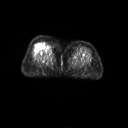
FDG PET of an extremity soft-tissue mass (from a PET/CT study), one axial slice; slice 23 of 267 in the series (ordered by position); 3.27 mm slice thickness; 128 × 128 image matrix, field of view 700 × 700 mm. Female patient, age 56 years. Case-level facts recorded for this patient, not image findings: histological type: malignant solitary fibrous tumor; grade: intermediate; site of the primary tumour: right thigh.
Outlined on this slice (expert contour drawn on MRI and transferred to this co-registered scan by the dataset authors):
- gross tumour volume including surrounding oedema: bounding box (x1, y1, x2, y2) in pixels: (38, 41, 54, 54)
- gross tumour volume (mass): (44, 45, 49, 50)